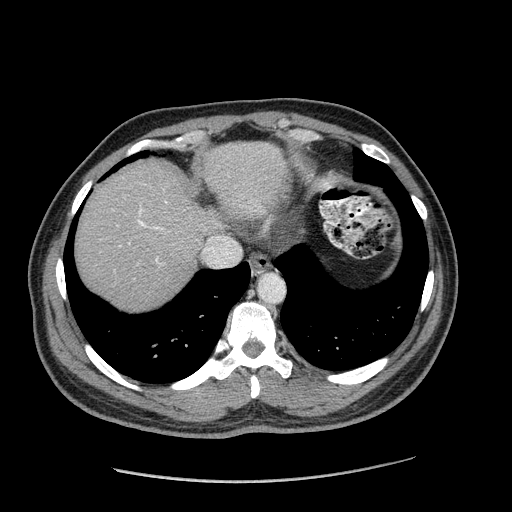
Contrast-enhanced abdominal CT (liver protocol), one axial slice; slice 155 of 182 in the series (ordered by position); reconstruction kernel STANDARD; 120 kVp; soft-tissue window (W 400 / L 40 HU); 2.5 mm slice thickness; 512 × 512 image matrix, field of view 400 × 400 mm. From the clinical record (not read from this slice): diagnosis: hepatocellular carcinoma (patient treated with transarterial chemoembolisation; whether this scan precedes or follows treatment is not stated here); TNM stage (as recorded): Stage-I; Child-Pugh class: A.
Outlined on this slice (semi-automatically segmented with operator editing):
- abdominal aorta: bounding box [x1, y1, x2, y2] px = [259, 274, 284, 303]
- liver parenchyma outside the tumour (the mass and vessels are separate outlines, so this box may not span the whole liver): [76, 142, 290, 310]
- liver vessels: [139, 211, 158, 261]